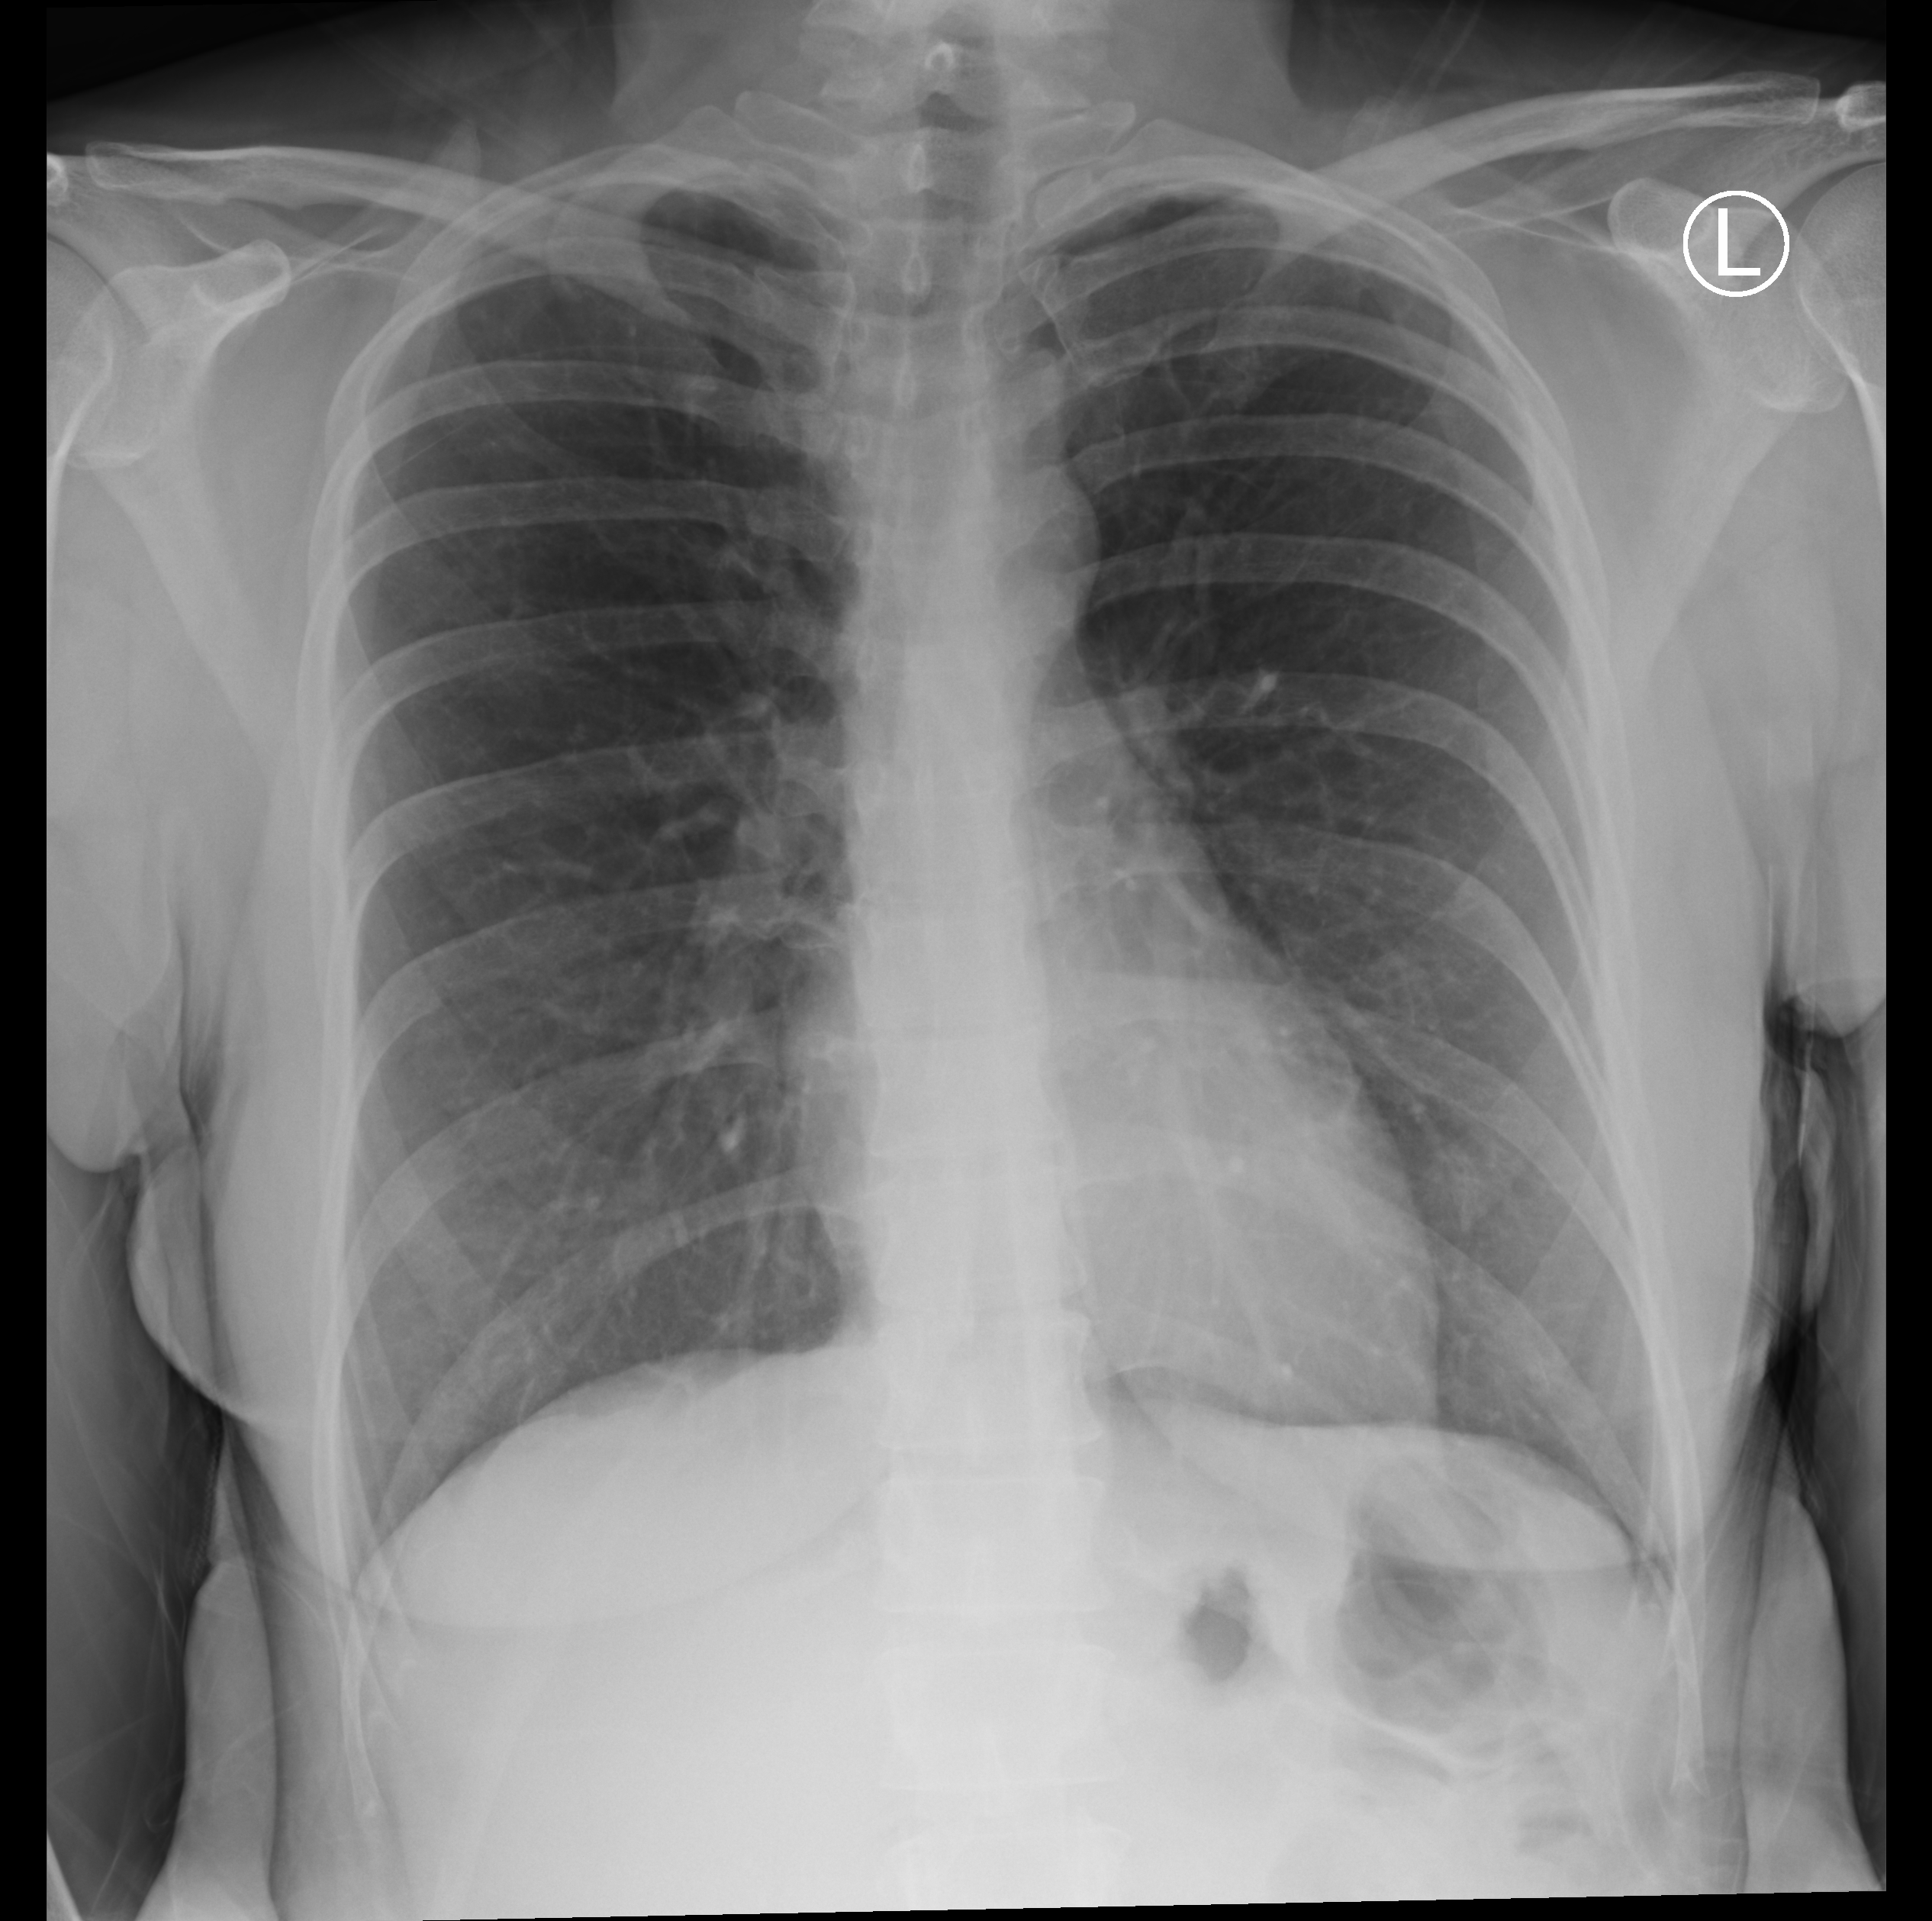
Bedside chest radiograph (computed radiography), anteroposterior (AP) projection. Female patient hospitalised with COVID-19, age 18–59 years.
Admission-level facts for this patient (not findings on this image; timing relative to this image not recorded):
- length of hospital stay: 1 day
- admitted to intensive care during this hospital stay: no